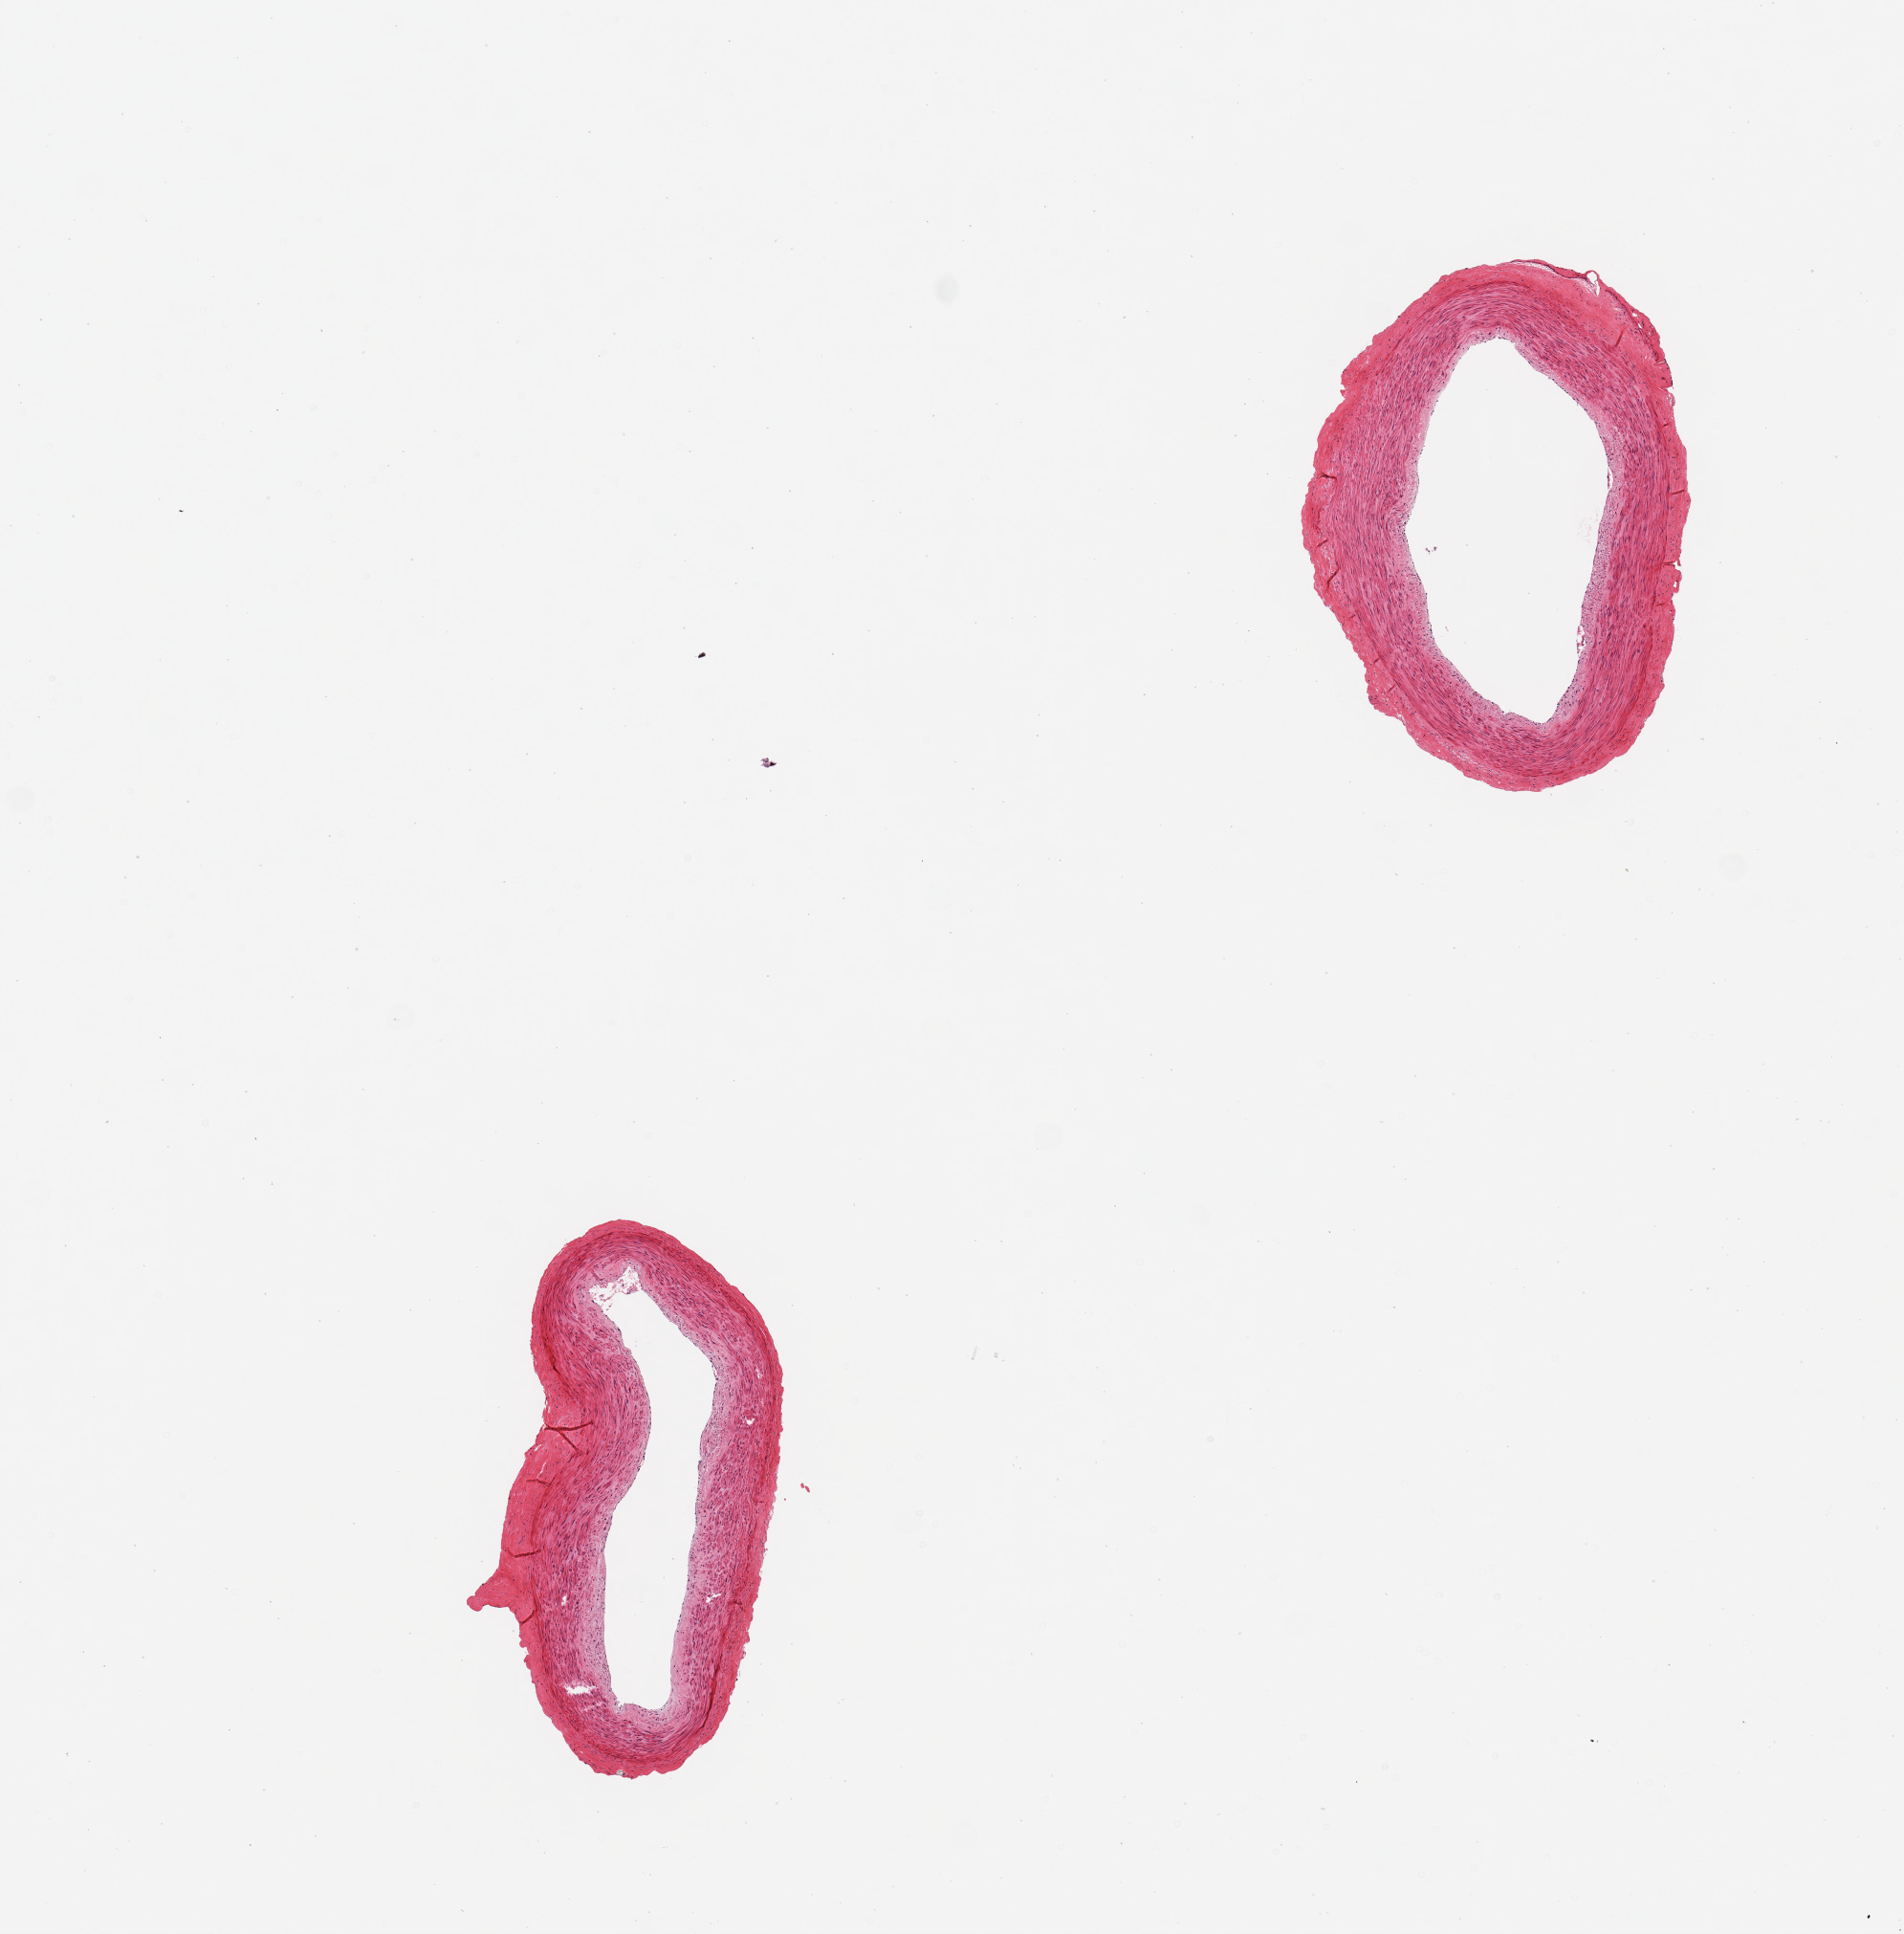
Whole-slide image, haematoxylin and eosin stain, whole scanned area (about 7.9 x 8.0 mm, acquisition: 20x scan) shown as a low-resolution overview. PAXgene-fixed paraffin-embedded (PFPE) section. Sampled site (target tissue): tibial artery. Donor tissue sample. Male donor.
• reviewer comment on this tissue sample: 2 pieces, minimal adherent fat